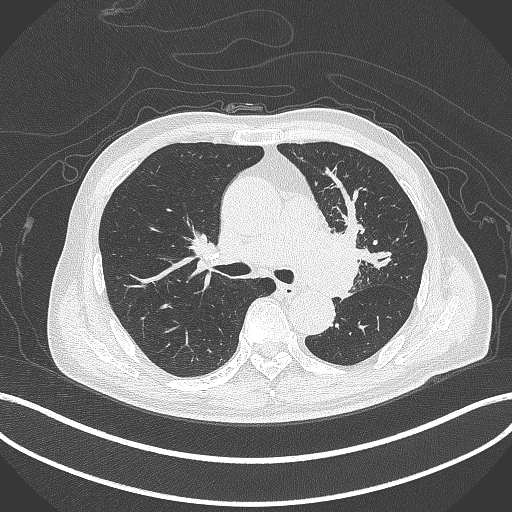
Chest CT, one axial slice; slice 268 of 417 in the series (ordered by position); lung window (W 1500 / L -600 HU); 1 mm slice thickness; 512 × 512 image matrix. Patient: male, 77 years. From the clinical record (not read from this slice): clinical TNM (as recorded): T3 N1 M0.
Annotated regions visible in this slice (bounding box drawn by a radiologist):
- lung tumour (recorded histology: adenocarcinoma): bounding box (x1, y1, x2, y2) in pixels: (318, 223, 372, 299)